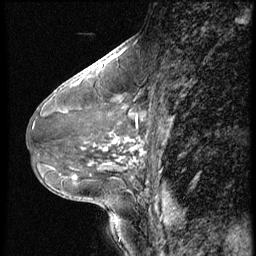
Breast MRI (dynamic contrast-enhanced), one sagittal slice. Position 26 of 56 along the scan axis. Dynamic contrast-enhanced series, image 2 of 3 at this slice position (ordered by acquisition). 1.5 T. TE 4.2 ms, TR 9 ms. 2.5 mm slice thickness. 256 × 256 image matrix. Female patient, age 46 years. Case-level facts recorded for this patient, not image findings: setting: breast cancer imaged before/during neoadjuvant chemotherapy; receptor status: HER2-positive.
Annotated regions visible in this slice (semi-automatically segmented with operator editing):
- analysis volume of interest (the breast-tissue region the enhancement analysis was run in; not a lesion): bounding box [x1, y1, x2, y2] px = [64, 98, 174, 182]
- tumour enhancement mask (voxels above the 140 % enhancement threshold inside the analysis volume of interest): [75, 137, 143, 178]